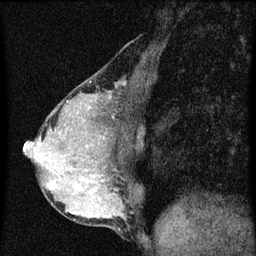
Breast MRI (dynamic contrast-enhanced), one sagittal slice. Position 23 of 60 along the scan axis. Dynamic contrast-enhanced series, image 2 of 3 at this slice position (ordered by acquisition). 1.5 T. TE 4.2 ms, TR 8 ms. 2 mm slice thickness. 256 × 256 image matrix, field of view 180 × 180 mm. Patient: female, 49 years.
Structures marked on this image (semi-automatically segmented with operator editing):
- analysis volume of interest (the breast-tissue region the enhancement analysis was run in; not a lesion): bounding box <44,174,89,201> (left, top, right, bottom; pixels)
- tumour enhancement mask (voxels above the 70 % enhancement threshold inside the analysis volume of interest): <50,182,80,191>